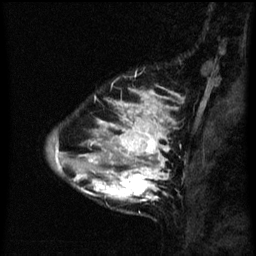
Breast MRI (dynamic contrast-enhanced), one sagittal slice. Position 16 of 60 along the scan axis. Dynamic contrast-enhanced series, image 2 of 3 at this slice position (ordered by acquisition). 1.5 T. TE 4.2 ms, TR 8 ms. 2.3 mm slice thickness. 256 × 256 image matrix. Female patient, age 33 years.
Annotated regions visible in this slice (semi-automatically segmented with operator editing):
- analysis volume of interest (the breast-tissue region the enhancement analysis was run in; not a lesion): box from (x=71, y=118) to (x=171, y=213) px
- tumour enhancement mask (voxels above the 70 % enhancement threshold inside the analysis volume of interest): (x=74, y=118)–(x=170, y=203)